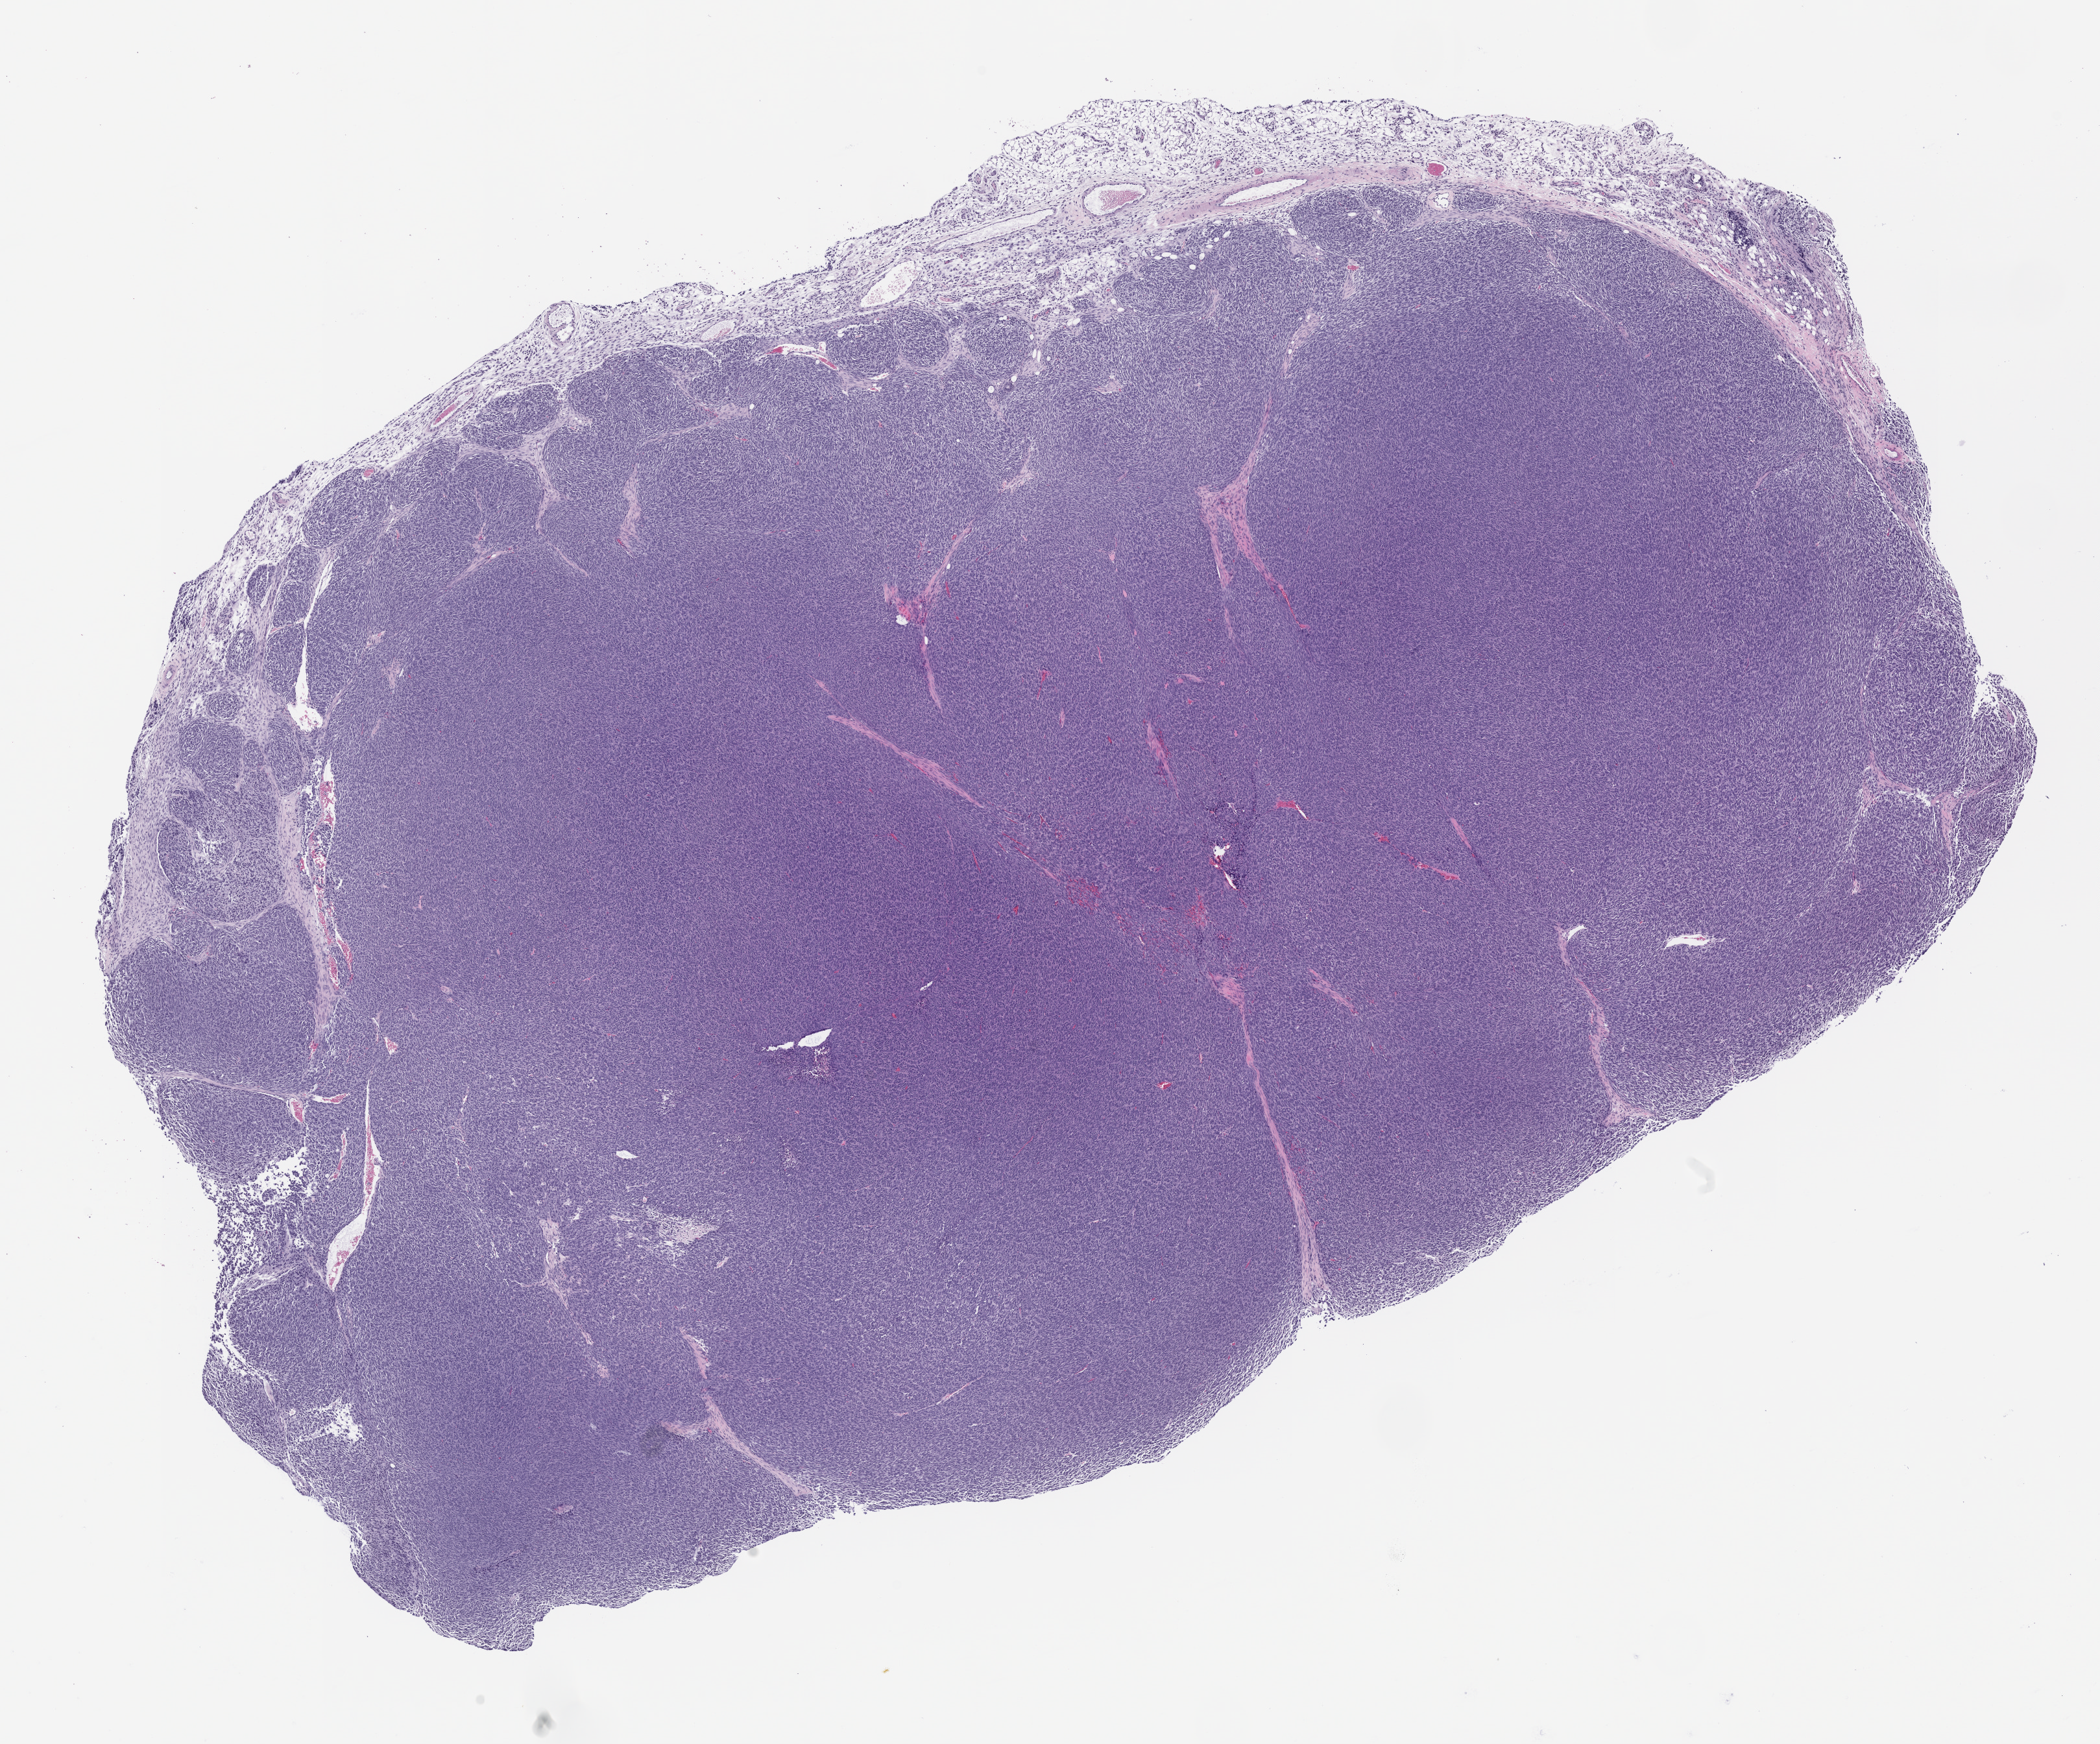
H&E whole-slide image of a patient-derived xenograft (PDX) tumor grown in a mouse, passage 2 — low-resolution overview of the scanned area, about 13.0 x 10.8 mm, formalin-fixed paraffin-embedded section, tumor site category: musculoskeletal.
Originating patient diagnosis: Synovial Sarcoma.